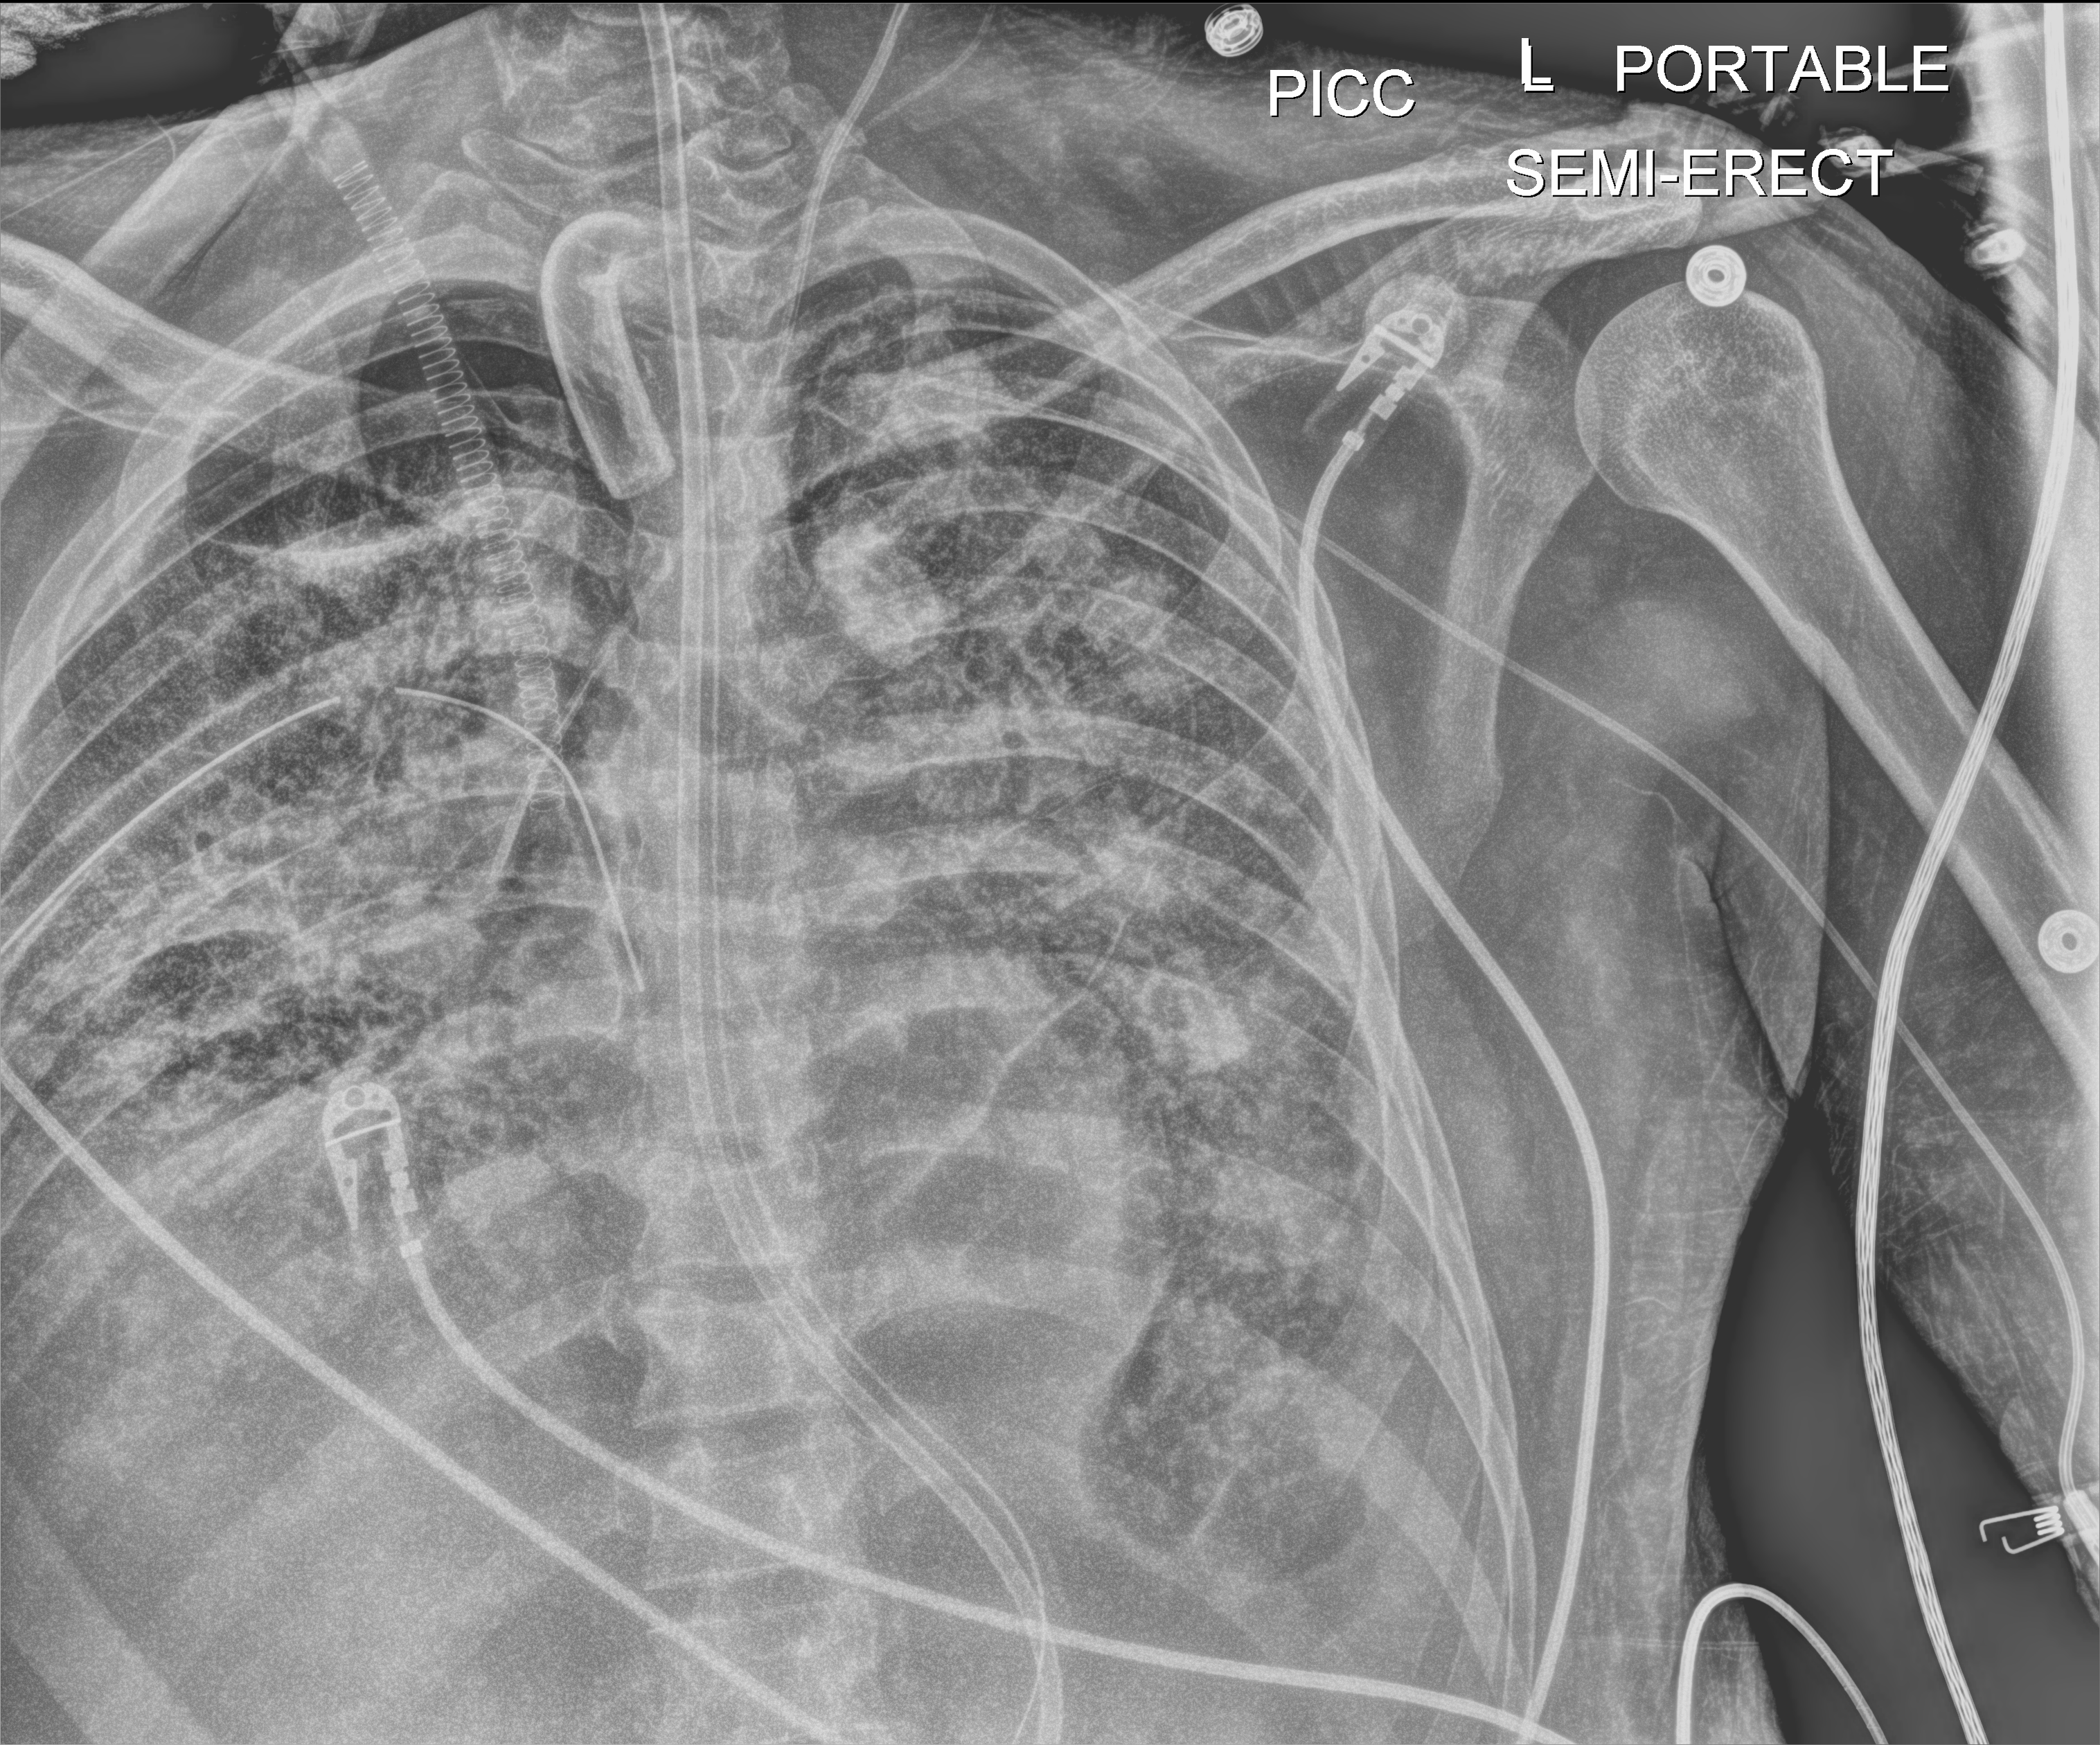
Portable chest radiograph, anteroposterior (AP) projection. Adult patient hospitalised with COVID-19, age 18–59 years.
Admission-level facts for this patient (not findings on this image; timing relative to this image not recorded): mechanically ventilated during this hospital stay: yes.